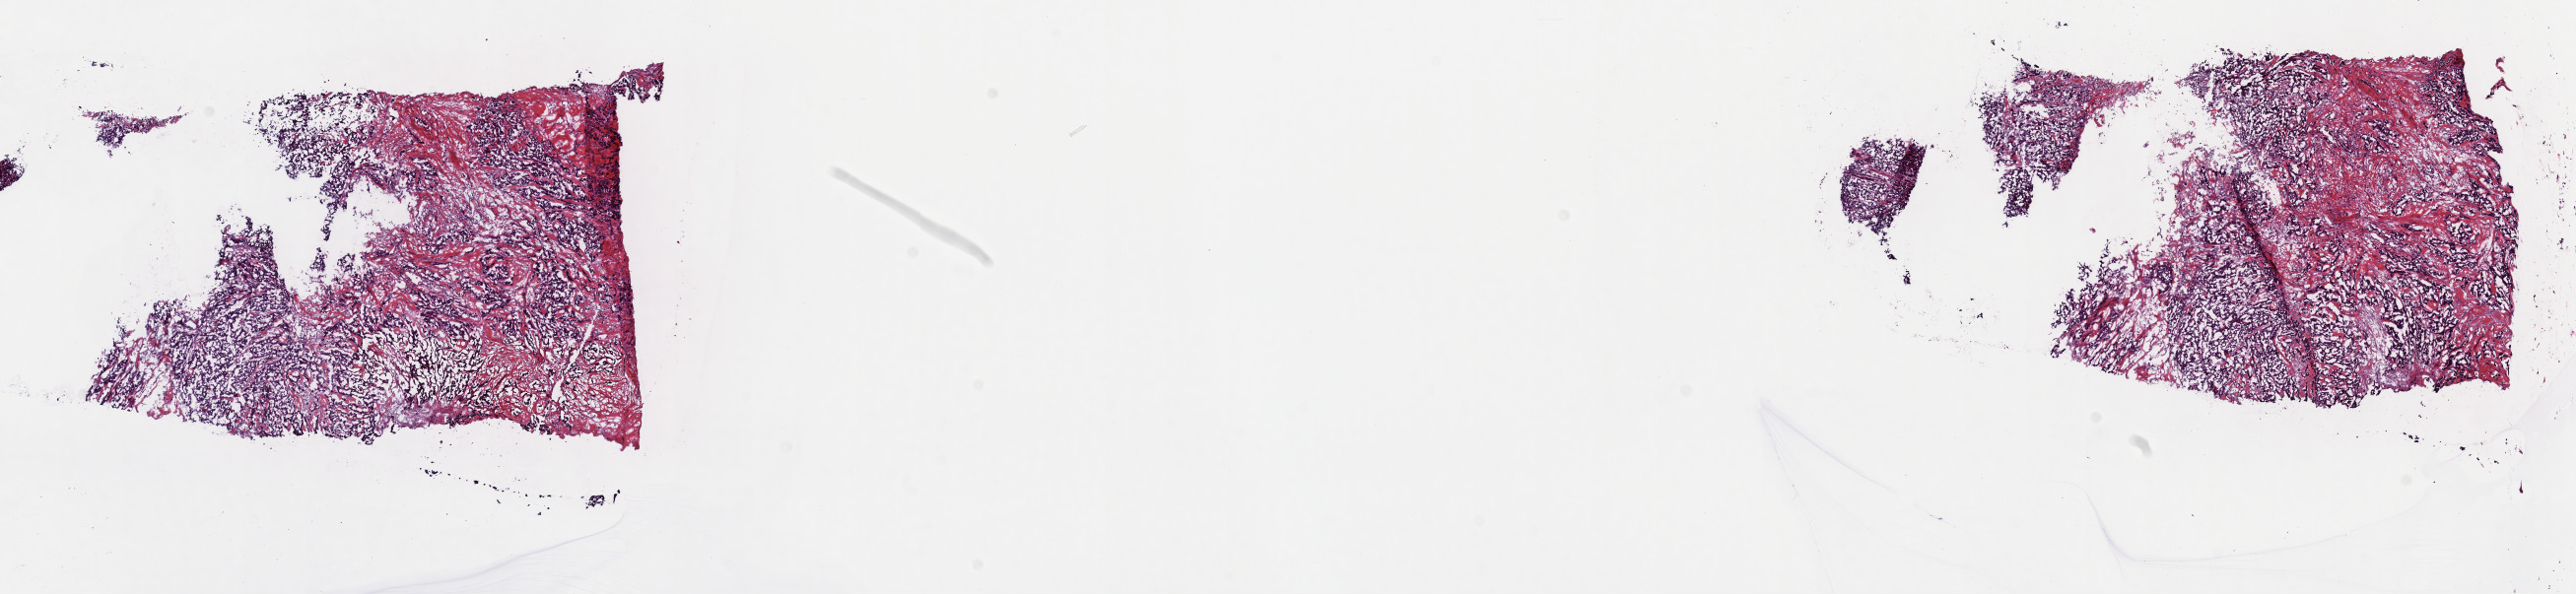
Digitized H&E-stained tissue section (whole slide), low-resolution overview of the scanned area, about 21.1 x 4.9 mm (acquisition: 40x scan), frozen section from the top of the tissue portion, primary tumour sample from the breast. Female patient; age at initial diagnosis 50 years. Composition of this section per pathologist review: tumour cells 60%, tumour nuclei 60%, normal cells 5%, stromal cells 35%, necrosis 0%. Infiltration values recorded for this section: lymphocyte infiltration 2%, monocyte infiltration 0%, neutrophil infiltration 0%.
AJCC pathologic stage: IIB. Pathologic diagnosis: Infiltrating duct carcinoma, NOS.